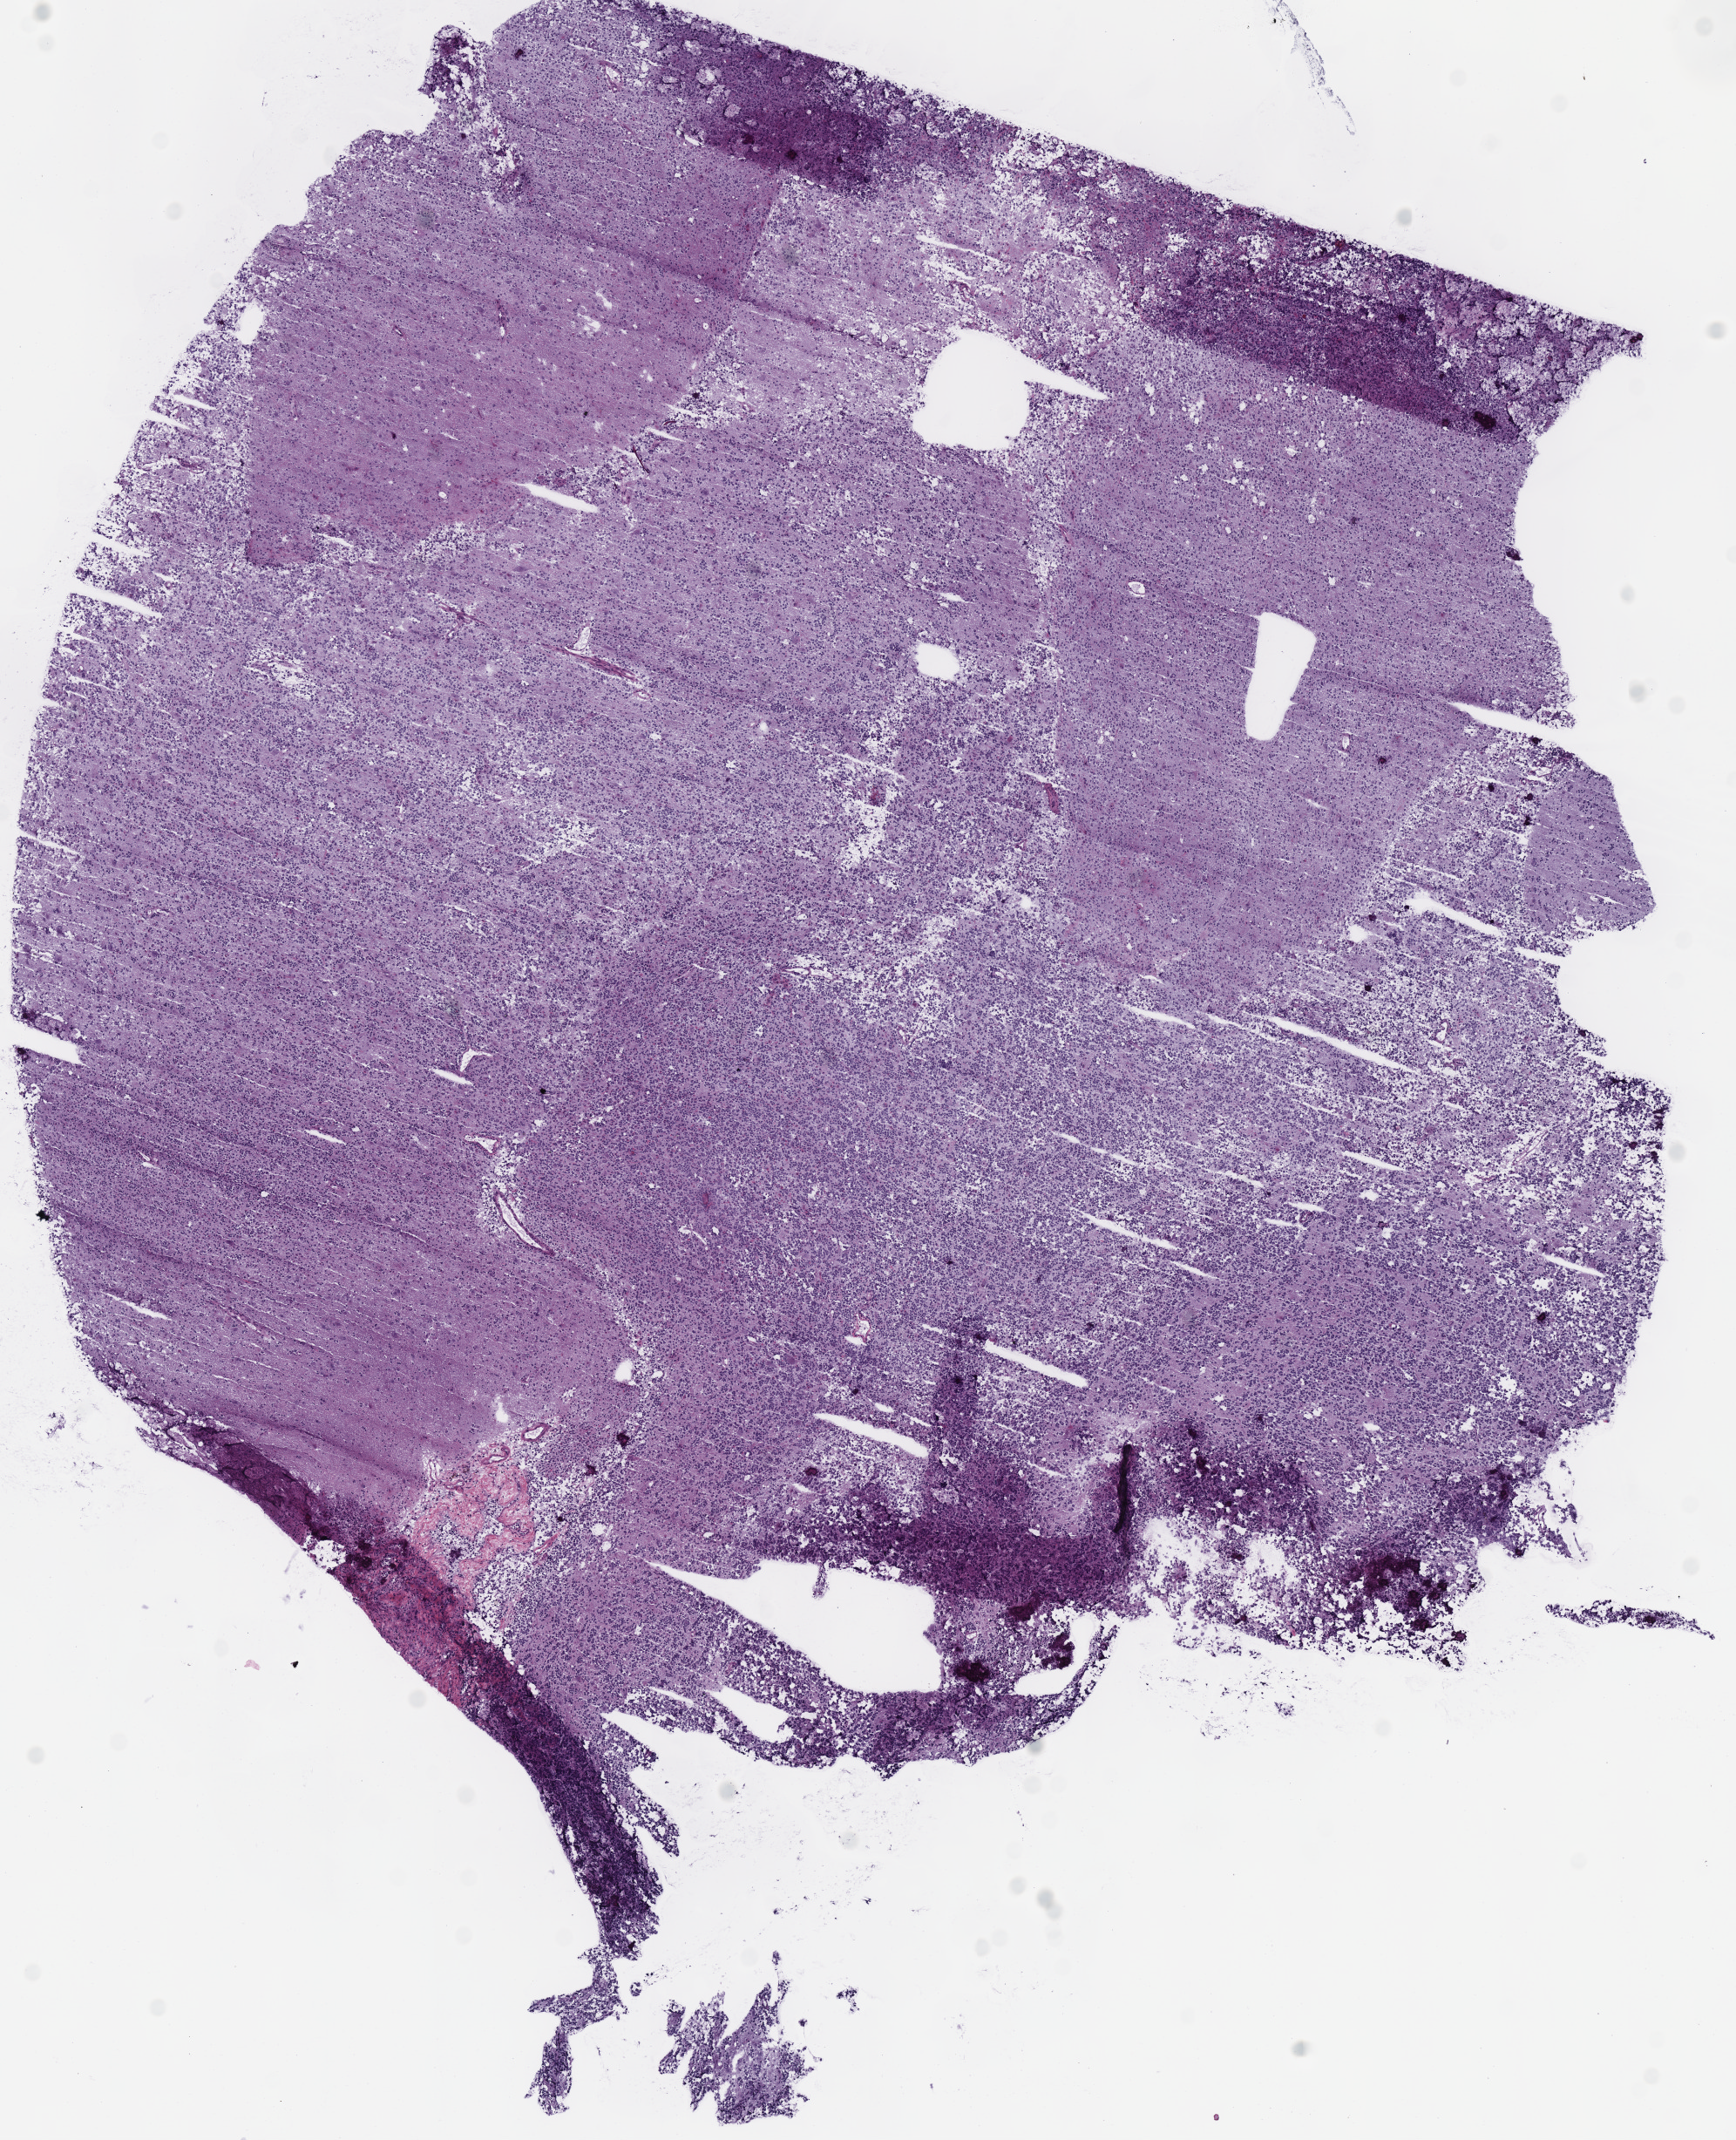
H&E whole-slide image — low-resolution overview of the scanned area, about 7.8 x 9.7 mm (from a 40x scan). Frozen section from the top of the tissue portion. Primary tumour sample from the brain. Patient: female, age at initial diagnosis 55 years. Histologic grade: G3 (poorly differentiated). Composition of this section per pathologist review: tumour cells 100%, tumour nuclei 85%, normal cells 0%, stromal cells 0%, necrosis 0%.
Laterality: right. Pathologic diagnosis: Oligodendroglioma, anaplastic (cerebrum).